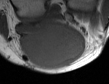
MRI of an extremity soft-tissue mass, one axial slice; position 19 of 50 along the scan axis; MR volume resampled by the dataset authors to the PET/CT grid (not the native acquisition matrix); 3.27 mm slice thickness; 109 × 84 image matrix. Male patient. Case-level facts recorded for this patient, not image findings: histological type: synovial sarcoma; site of the primary tumour: left poplietal fossa.
Structures marked on this image (expert contour drawn on MRI and transferred to this co-registered scan by the dataset authors):
- gross tumour volume (mass): bounding box (x1, y1, x2, y2) in pixels: (18, 26, 85, 68)